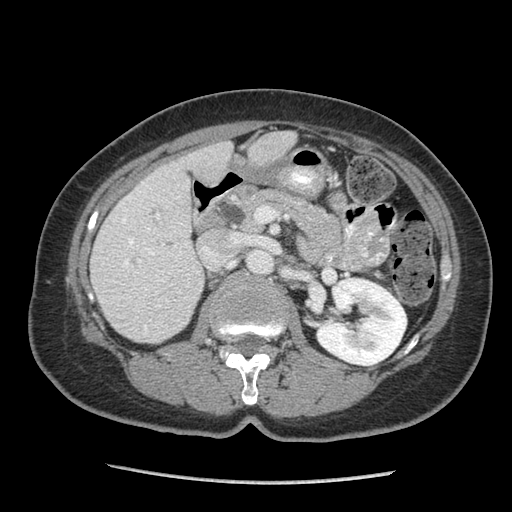
Contrast-enhanced abdominal CT (liver protocol), one axial slice. Slice 36 of 105 in the series (ordered by position). Reconstruction kernel STANDARD. Soft-tissue window (W 400 / L 40 HU). 2.5 mm slice thickness. 512 × 512 image matrix, field of view 340 × 340 mm. From the clinical record (not read from this slice): diagnosis: hepatocellular carcinoma (patient treated with transarterial chemoembolisation; whether this scan precedes or follows treatment is not stated here); TNM stage (as recorded): Stage-I; Child-Pugh class: A.
Structures marked on this image (semi-automatically segmented with operator editing):
- liver parenchyma outside the tumour (the mass and vessels are separate outlines, so this box may not span the whole liver): box from (x=90, y=130) to (x=296, y=342) px
- liver vessels: (x=115, y=183)–(x=179, y=330)